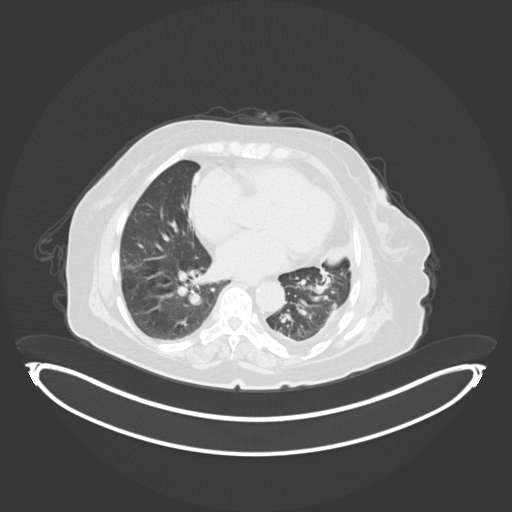
Chest CT, one axial slice. Lung window (W 1500 / L -600 HU). 512 × 512 image matrix, field of view 500 × 500 mm. Patient: female, 75 years. Case-level facts recorded for this patient, not image findings: clinical TNM (as recorded): T3 N3 M1.
Annotated regions visible in this slice (rectangle marked by the reading radiologist):
- lung tumour (recorded histology: adenocarcinoma): bounding box <325,243,356,269> (left, top, right, bottom; pixels)